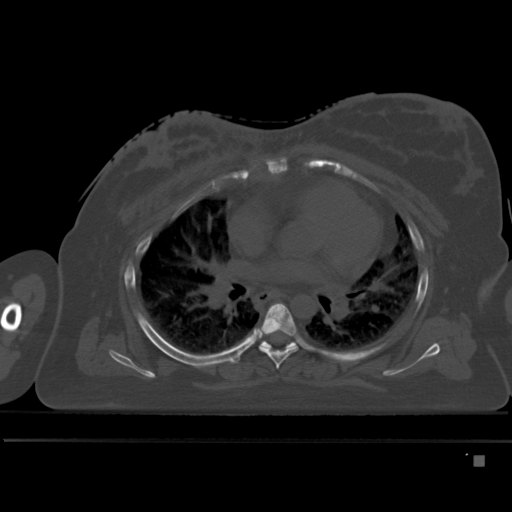
CT including the spine, one axial slice. Slice 315 of 495 in the series (ordered by position). Bone window (W 1800 / L 400 HU). 512 × 512 image matrix, field of view 404 × 404 mm. Female patient, age 33 years. Case-level facts recorded for this patient, not image findings: primary cancer: breast; vertebrae with lytic lesions (as recorded): T1.
Annotated regions visible in this slice (semi-automatic segmentation, software-assisted and operator-edited):
- T5 vertebra: bounding box [x1, y1, x2, y2] px = [260, 303, 298, 370]
- T6 vertebra: [260, 341, 299, 349]